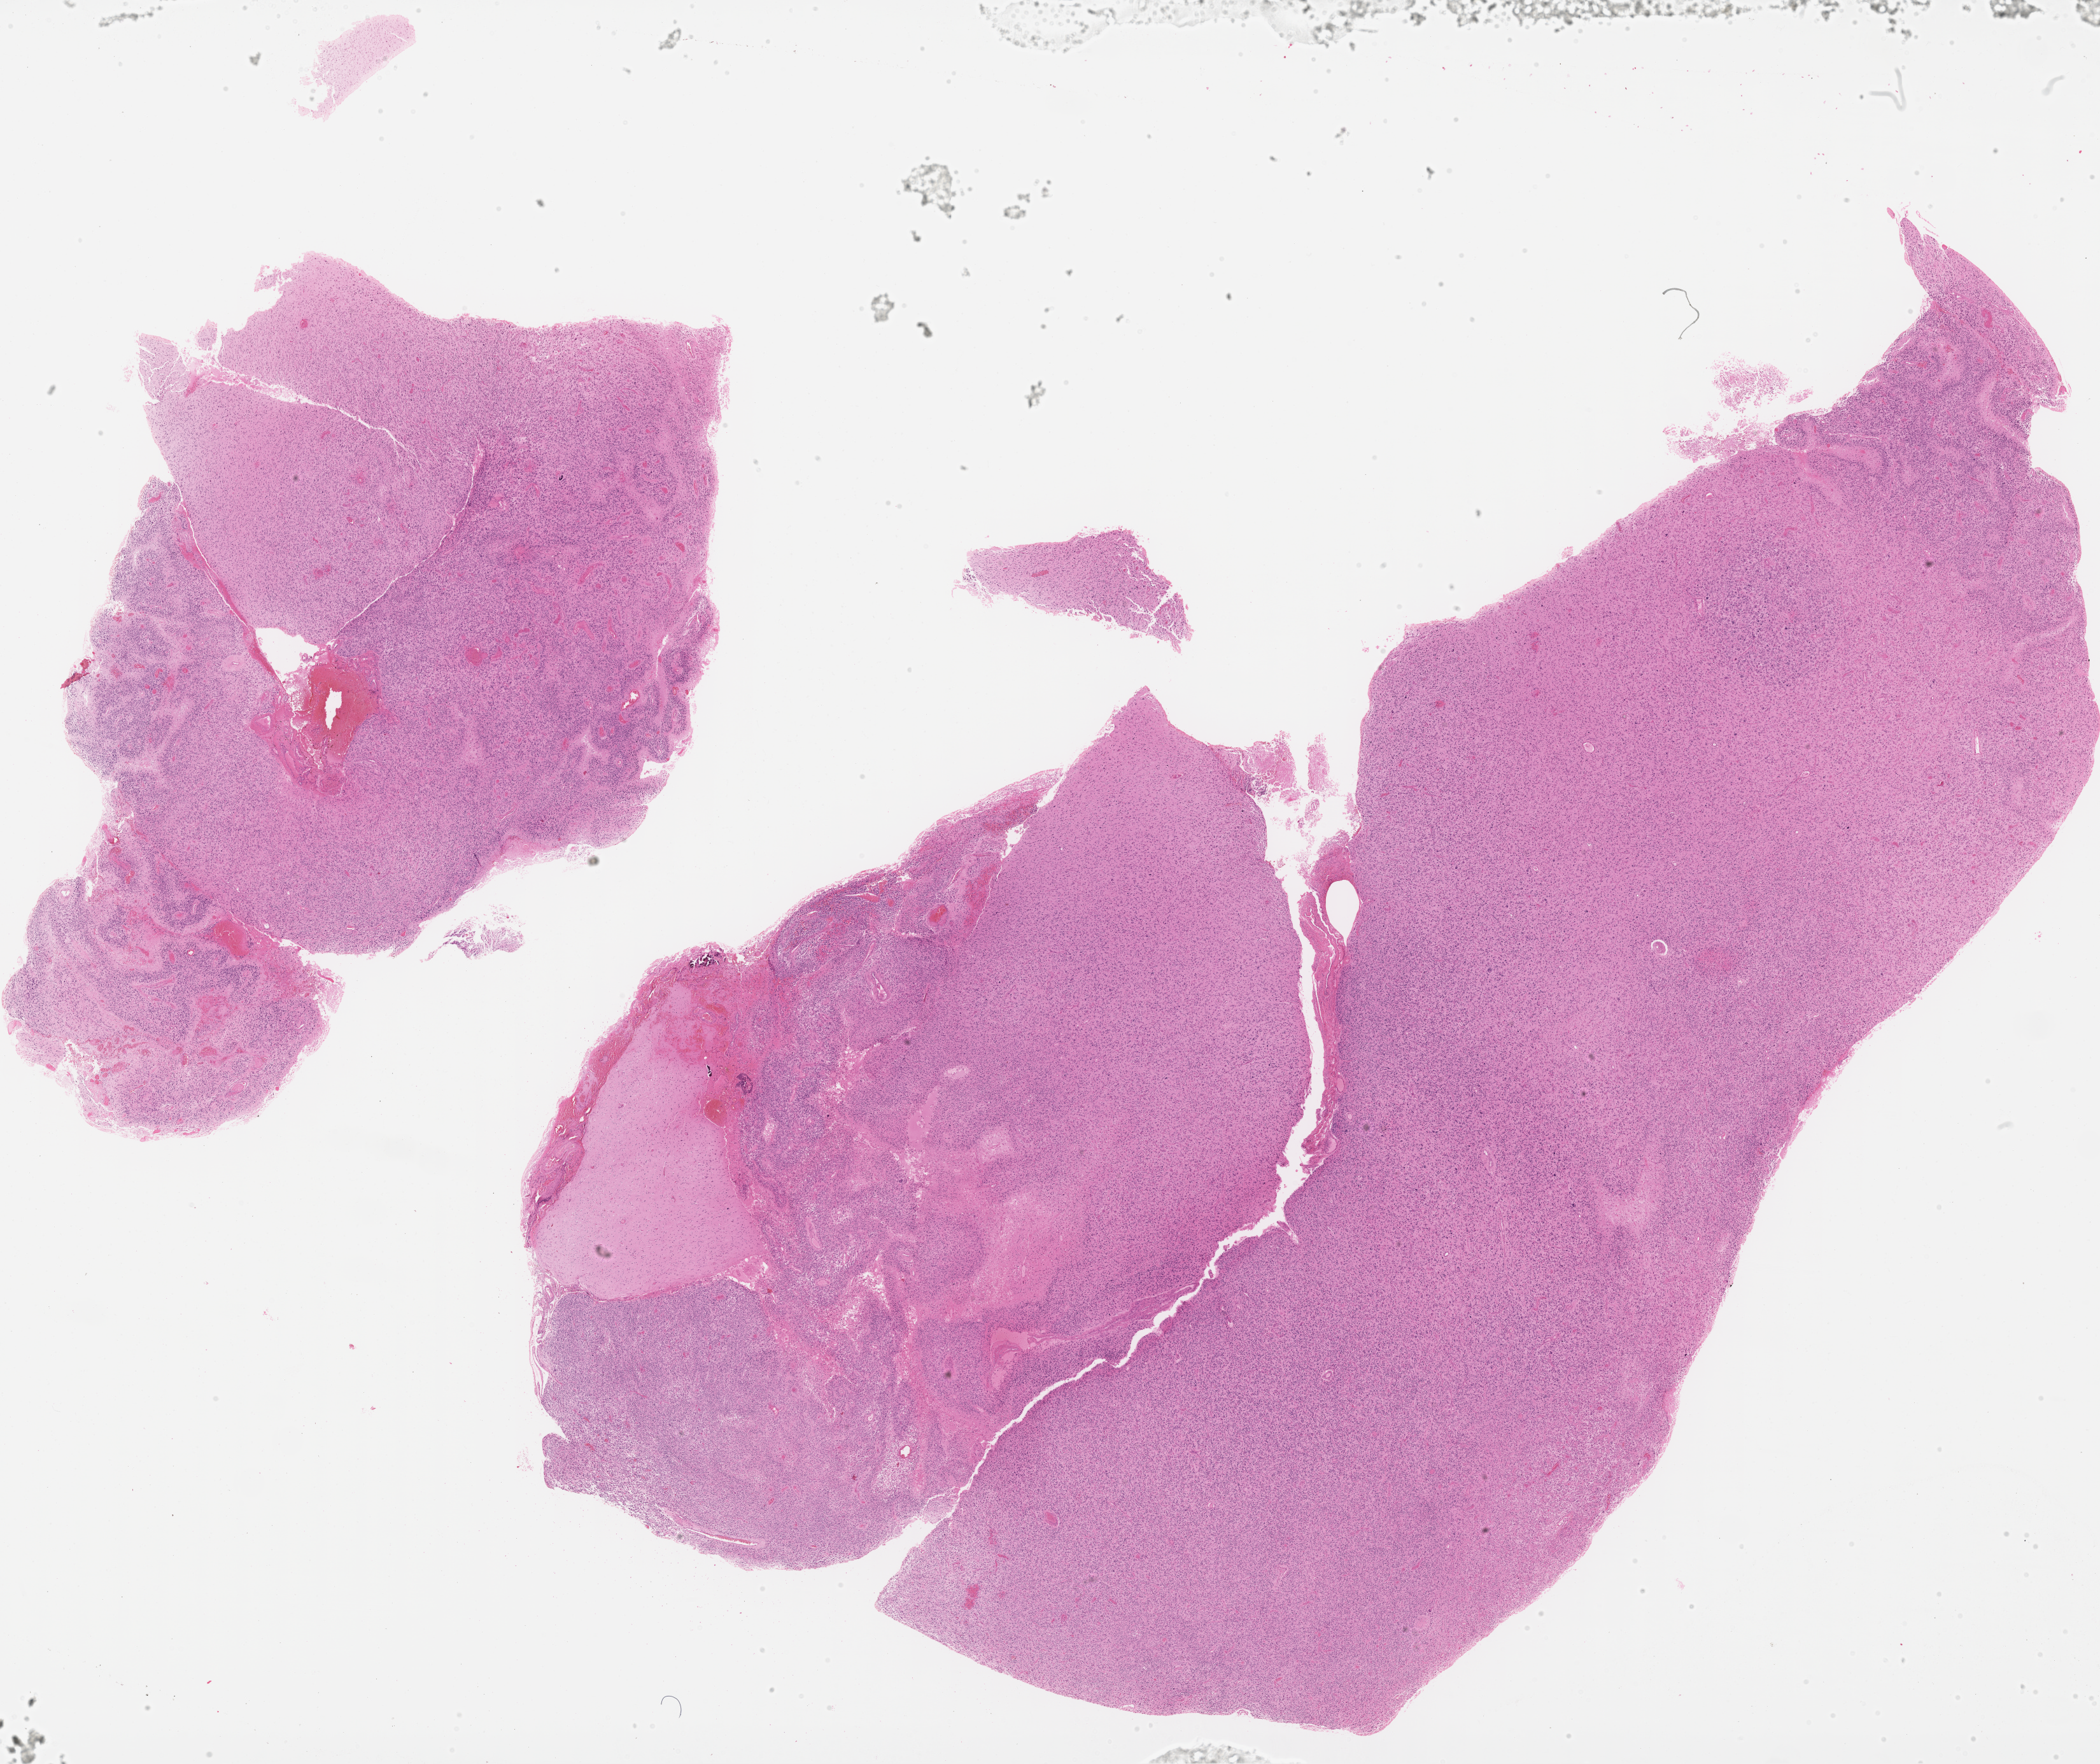
Whole-slide histology image, Hematoxylin and eosin (H&E) stained, whole scanned area (about 26.7 x 22.5 mm, acquisition: 40x scan) shown as a low-resolution overview; formalin-fixed paraffin-embedded (FFPE) diagnostic section; brain, primary tumour sample. Patient: male, age at initial diagnosis 80 years.
Diagnosis: Glioblastoma.